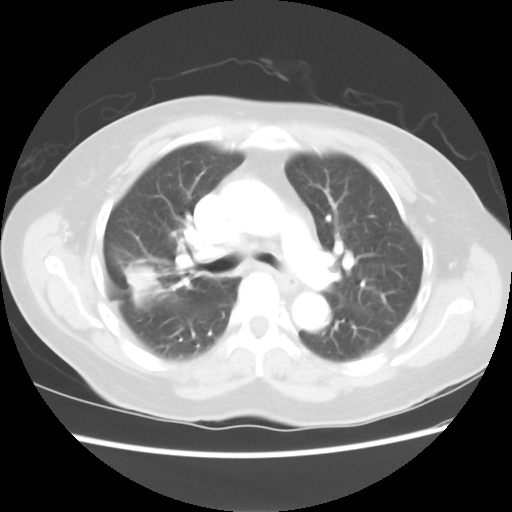
Chest CT, one axial slice. Slice 44 of 80 in the series (ordered by position). Reconstruction kernel STANDARD. 100 kVp. Lung window (W 1500 / L -600 HU). 5 mm slice thickness. 512 × 512 image matrix, field of view 342 × 342 mm. Female patient, age 67 years. Case-level facts recorded for this patient, not image findings: clinical TNM (as recorded): T1c N1 M0.
Annotated regions visible in this slice (rectangle marked by the reading radiologist):
- lung tumour (recorded histology: adenocarcinoma): box from (x=119, y=250) to (x=174, y=318) px